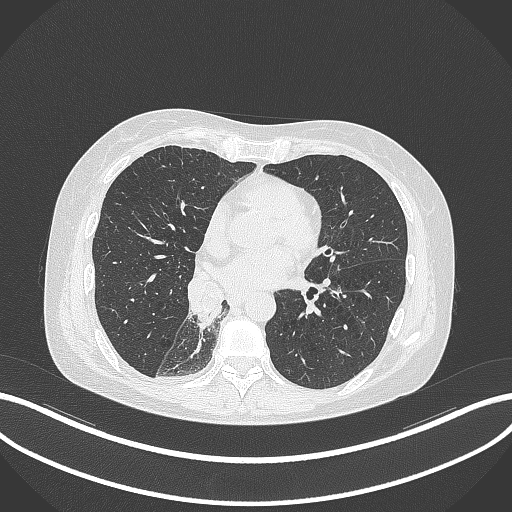
Chest CT, one axial slice. Position 138 of 329 along the scan axis. 120 kVp. Lung window (W 1500 / L -600 HU). 1 mm slice thickness. 512 × 512 image matrix, field of view 400 × 400 mm. Female patient, age 63 years. From the clinical record (not read from this slice): clinical TNM (as recorded): T1c N0 M0.
Outlined on this slice (rectangle marked by the reading radiologist):
- lung tumour (recorded histology: adenocarcinoma): bounding box <186,272,223,329> (left, top, right, bottom; pixels)